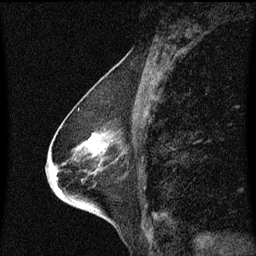
Breast MRI (dynamic contrast-enhanced), one sagittal slice. Position 29 of 60 along the scan axis. Dynamic contrast-enhanced series, image 2 of 3 at this slice position (ordered by acquisition). 1.5 T. TE 4.2 ms, TR 8.4 ms. 2 mm slice thickness. 256 × 256 image matrix, field of view 200 × 200 mm. Patient: female, 68 years. From the clinical record (not read from this slice): setting: breast cancer imaged before/during neoadjuvant chemotherapy; receptor status: triple-negative.
Structures marked on this image (semi-automatically segmented with operator editing):
- analysis volume of interest (the breast-tissue region the enhancement analysis was run in; not a lesion): bounding box [x1, y1, x2, y2] px = [44, 114, 126, 203]
- tumour enhancement mask (voxels above the 70 % enhancement threshold inside the analysis volume of interest): [55, 144, 102, 179]